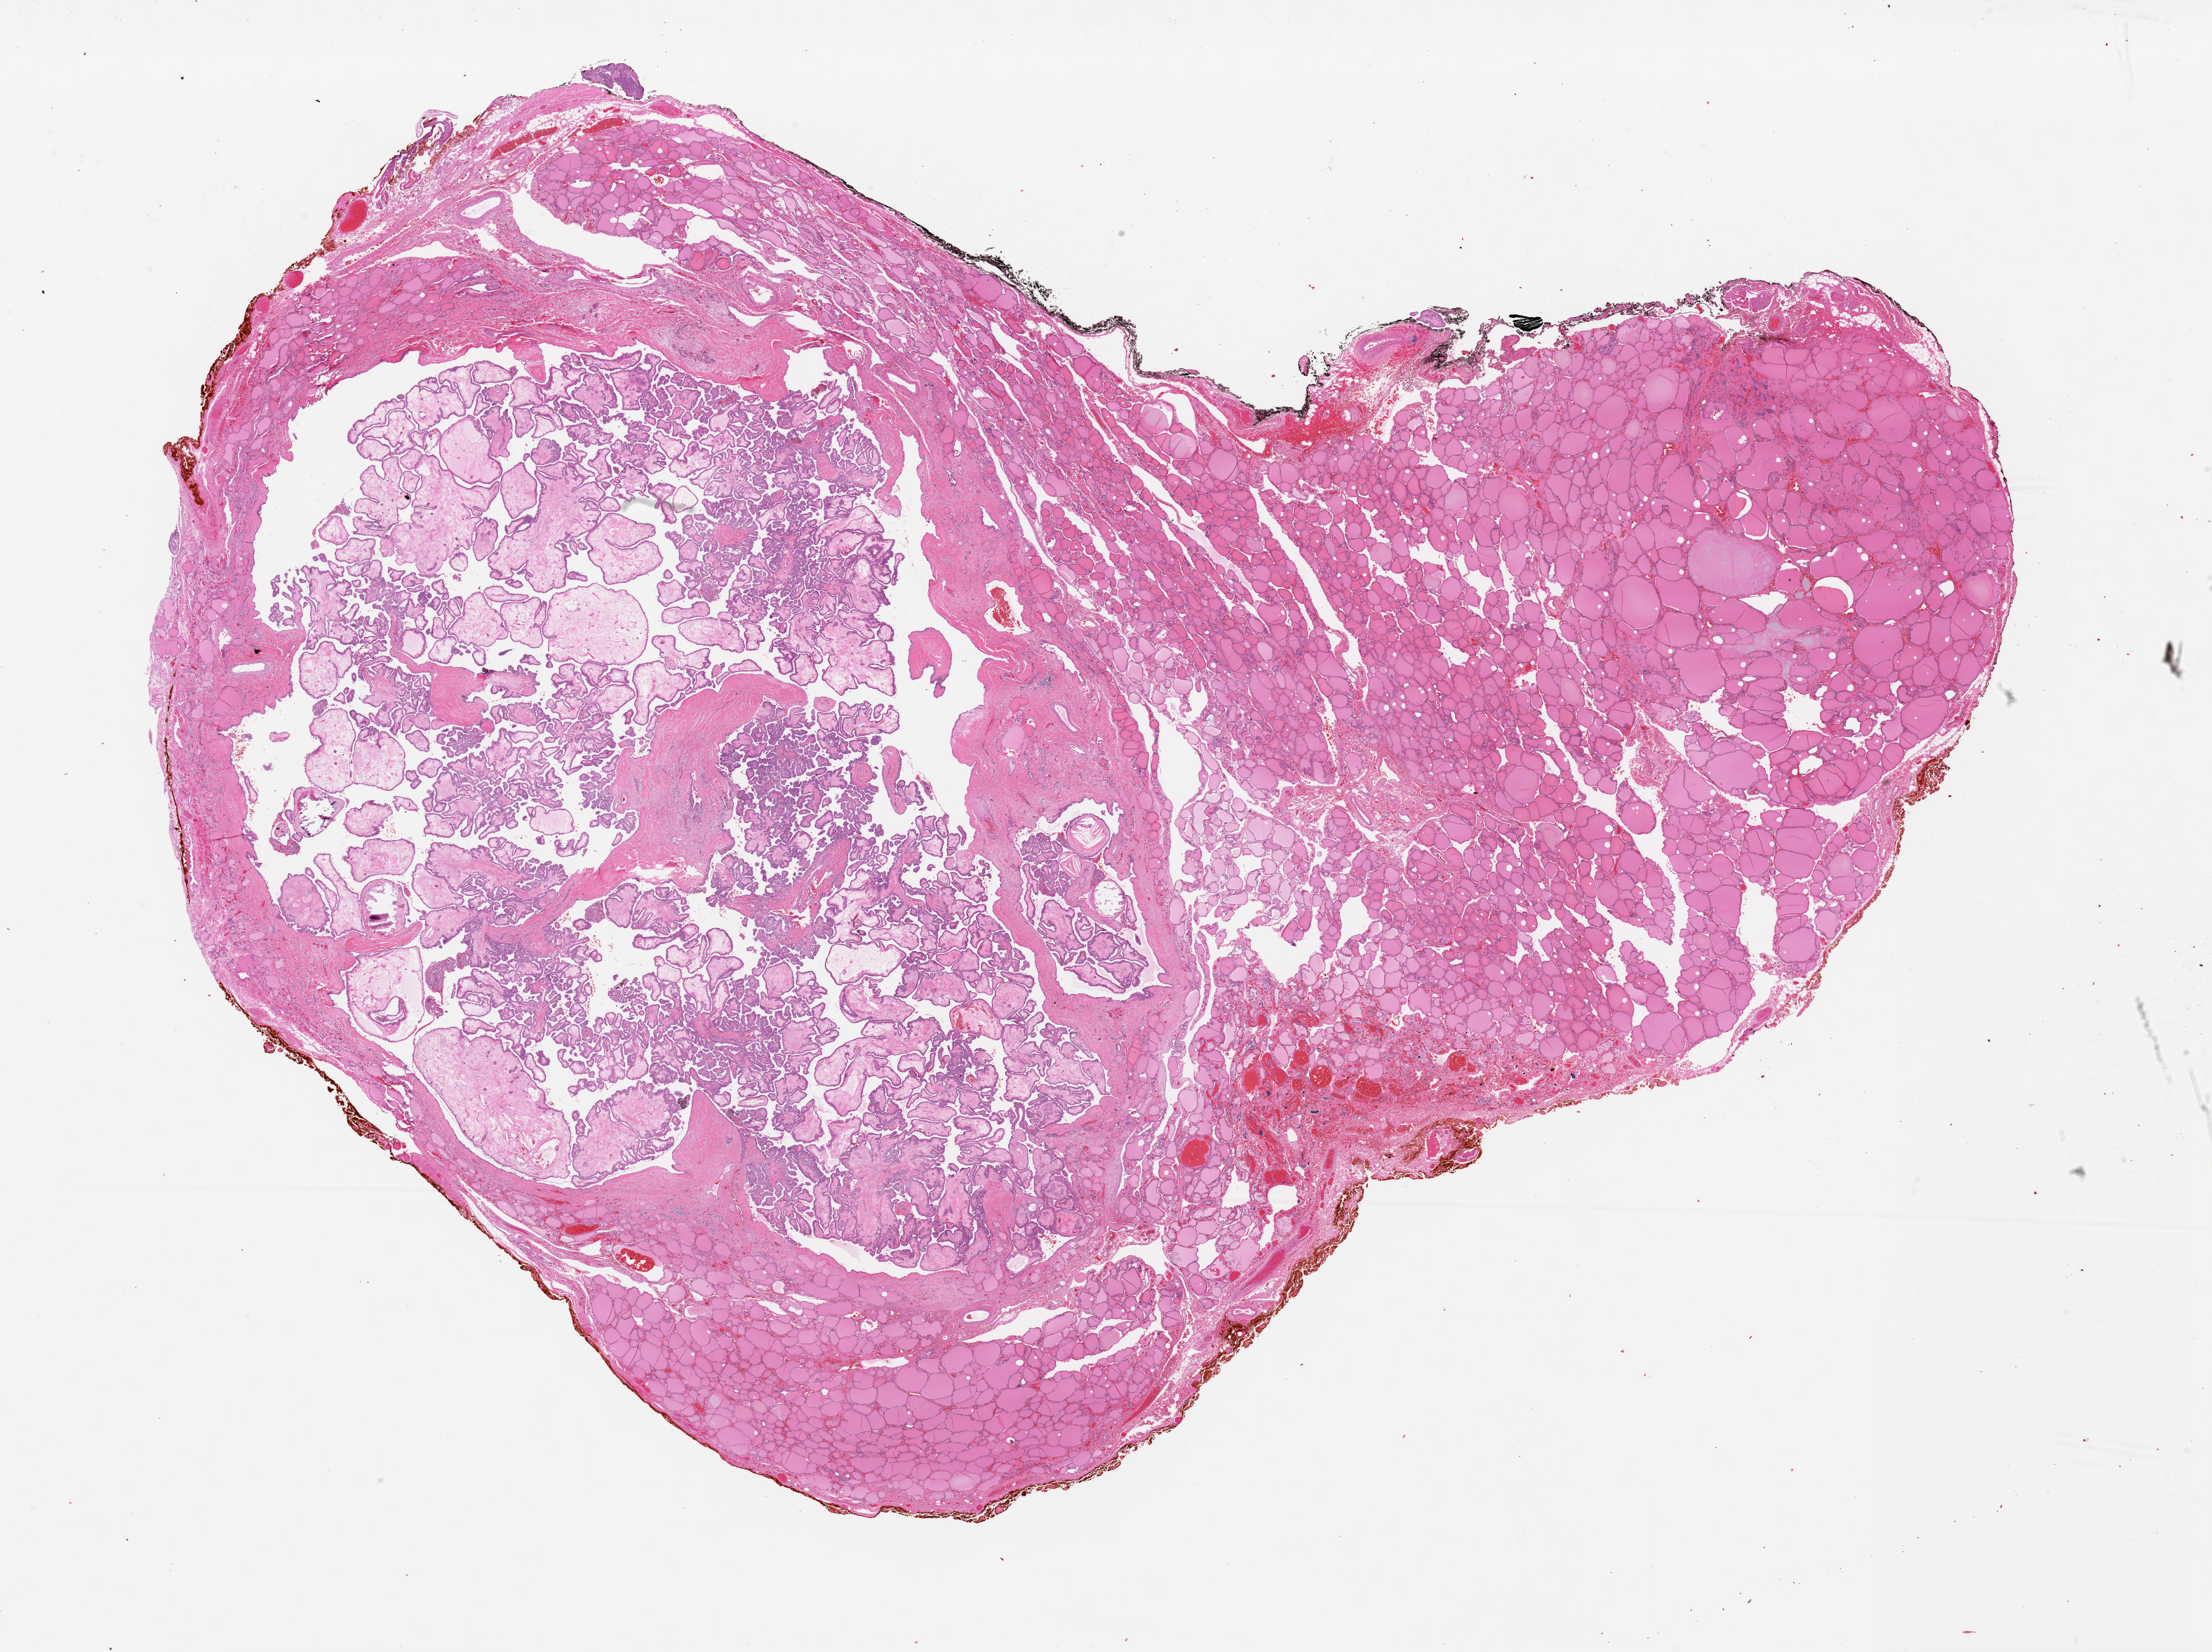
Digitized Hematoxylin and eosin (H&E) stained tissue section (whole slide) — a low-resolution overview of the entire scanned area, about 24.9 x 18.6 mm (acquisition: 40x scan), formalin-fixed paraffin-embedded (FFPE) diagnostic section, sample: primary tumour, thyroid. Female, age 33 years at initial diagnosis.
• AJCC pathologic stage: I (6th edition)
• laterality: right
• diagnosis: Papillary adenocarcinoma, NOS
• TNM: T2 NX MX